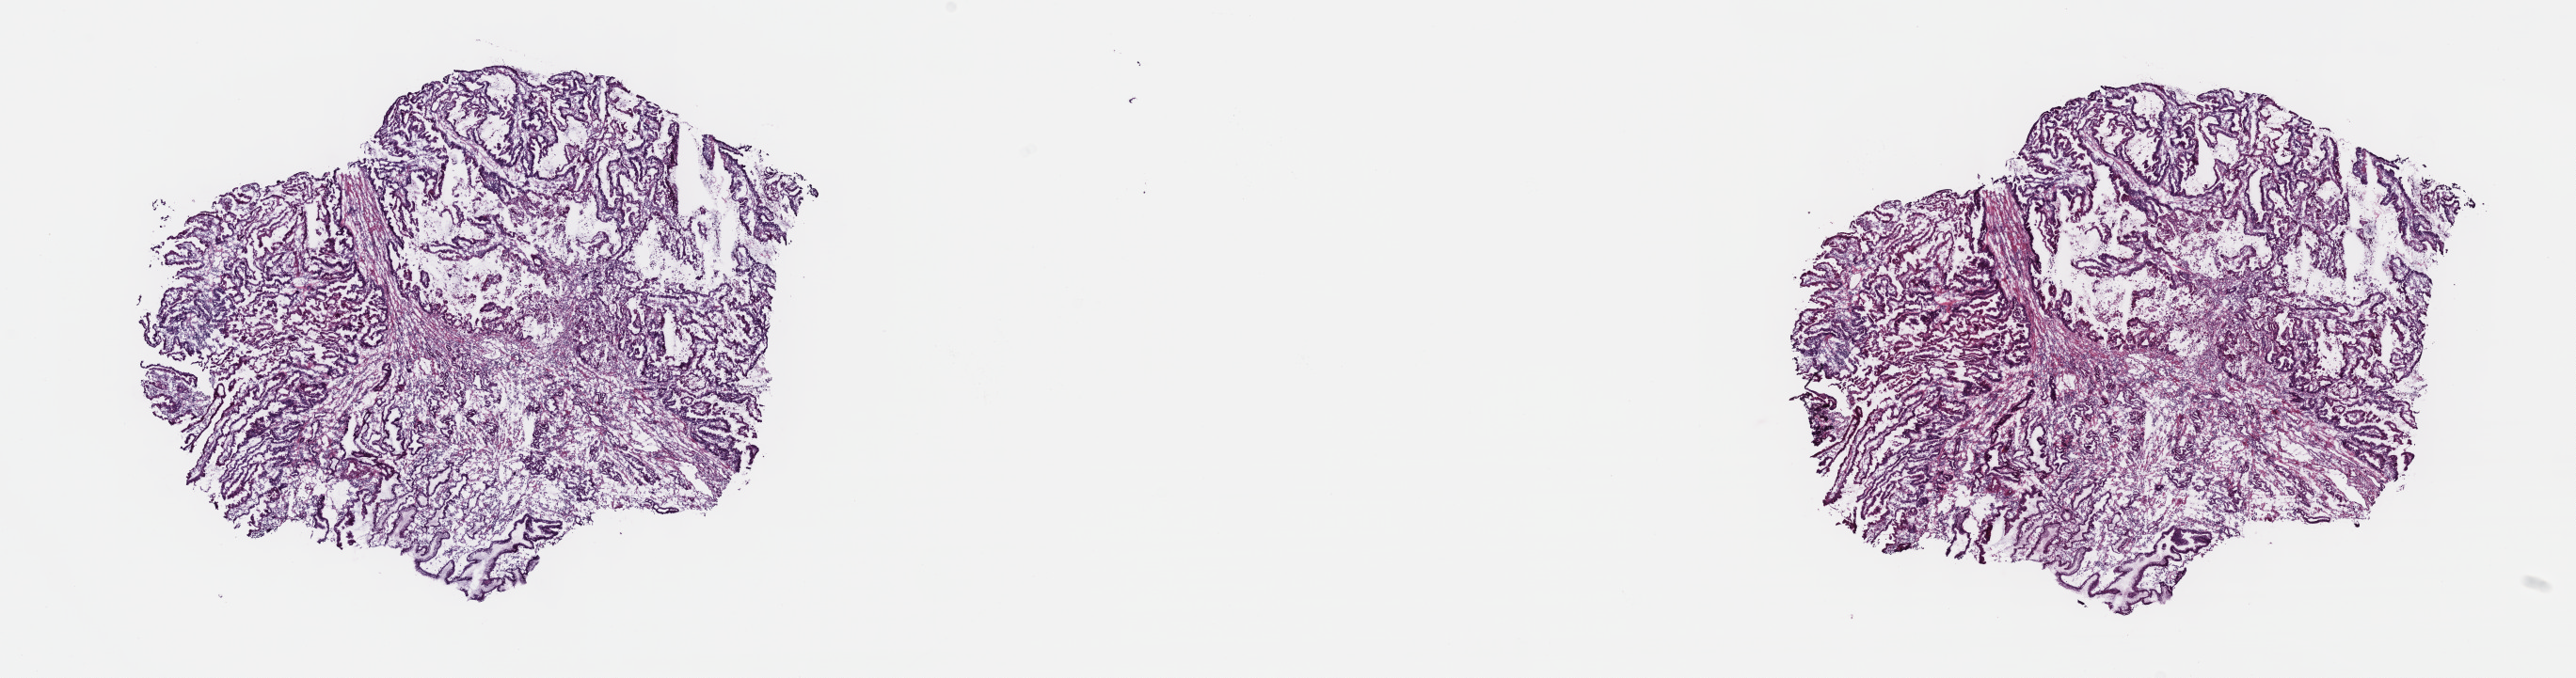
Hematoxylin and eosin (H&E) stained whole-slide image — whole scanned area (about 22.1 x 5.8 mm, from a 40x scan) shown as a low-resolution overview, frozen section from the top of the tissue portion, stomach, primary tumour sample. Patient: male, age at initial diagnosis 68 years. Histologic grade: G2 (moderately differentiated). Slide review estimates, as recorded: tumour cells 100%, tumour nuclei 60%, normal cells 0%, stromal cells 0%, necrosis 0%. Inflammatory infiltration, as recorded: lymphocyte infiltration 5%, monocyte infiltration 0%, neutrophil infiltration 0%.
• pathologic diagnosis: Adenocarcinoma, intestinal type (cardia, NOS)
• AJCC pathologic stage: IIA
• lymph nodes positive (case pathology): 0 of 19 examined